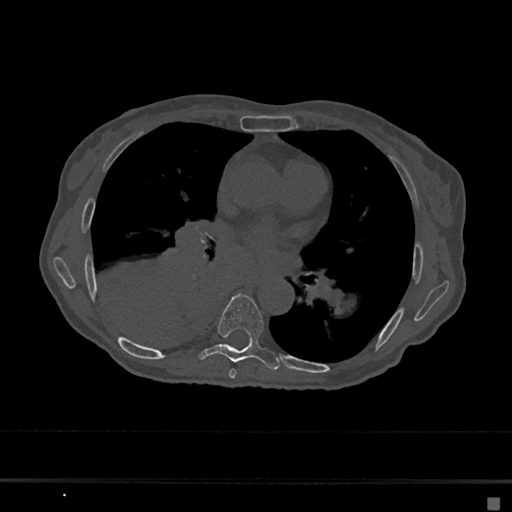
CT including the spine, one axial slice. Position 375 of 797 along the scan axis. Reconstruction kernel Br40s/3. Bone window (W 1800 / L 400 HU). 0.5 mm slice thickness. 512 × 512 image matrix, field of view 360 × 360 mm. Patient: female, 68 years. From the clinical record (not read from this slice): primary cancer: renal.
Structures marked on this image (semi-automatically segmented with operator editing):
- T6 vertebra: box from (x=228, y=369) to (x=236, y=379) px
- T7 vertebra: (x=198, y=294)–(x=280, y=370)